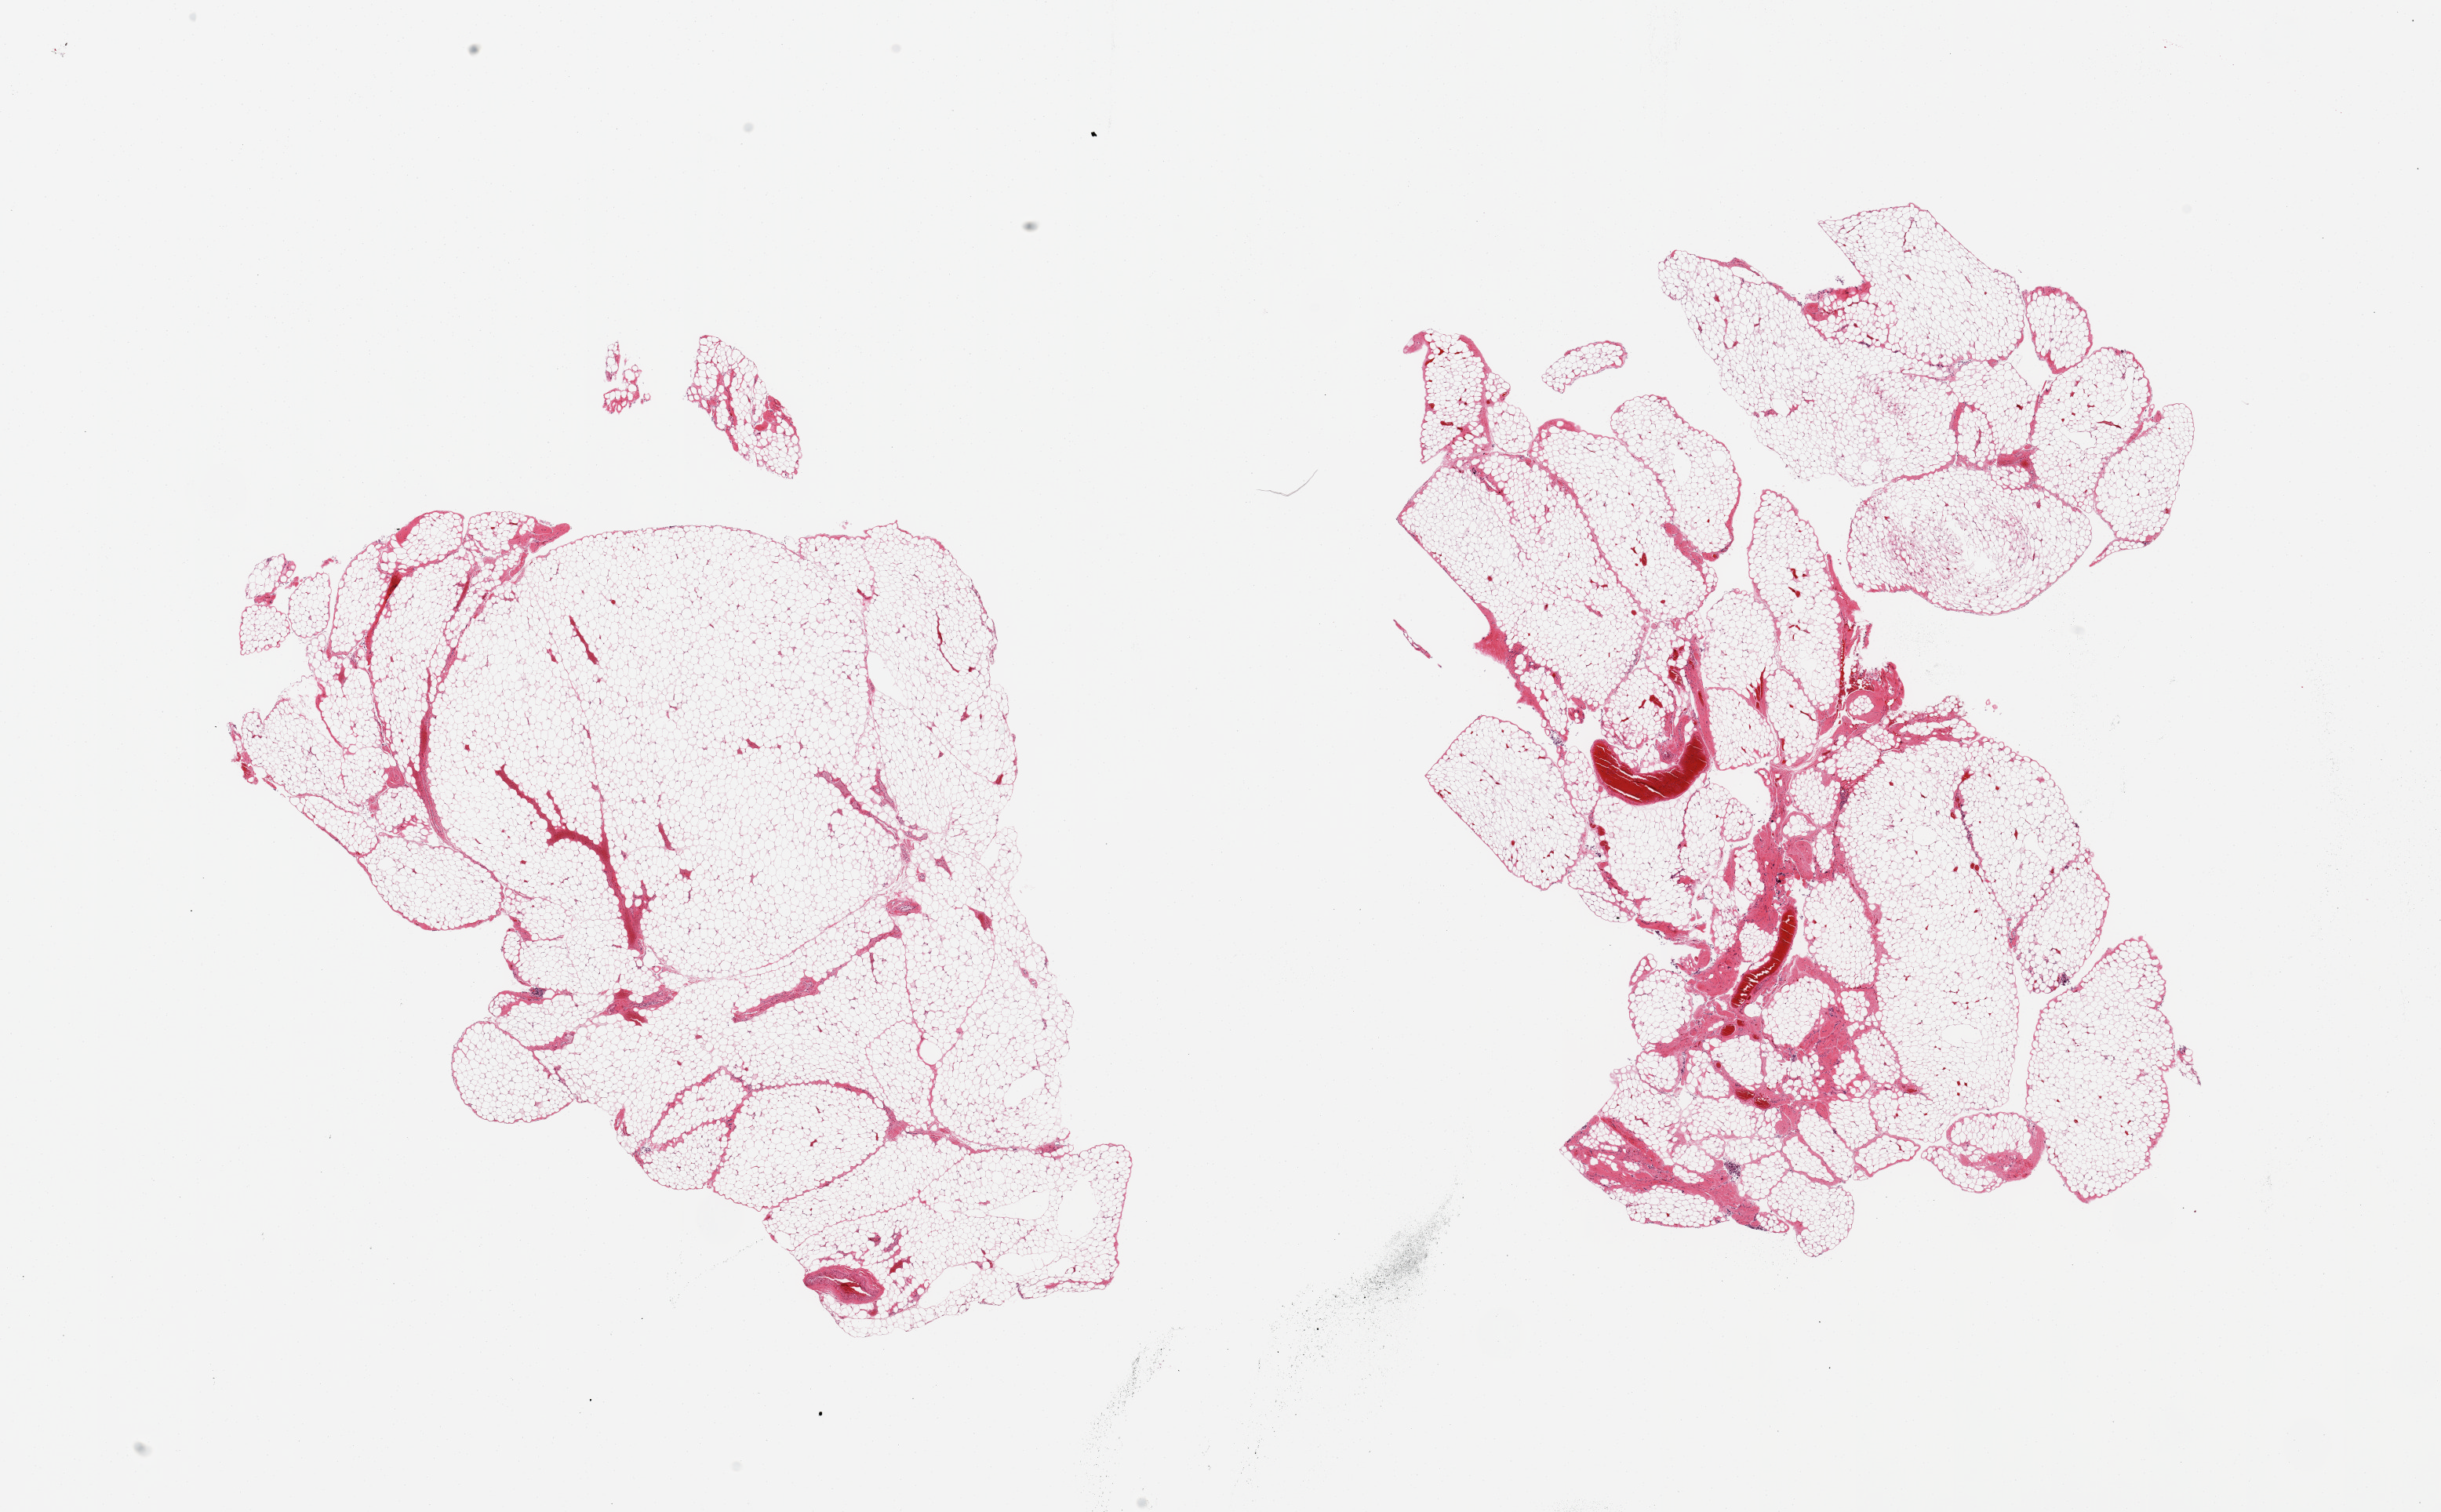
Hematoxylin and eosin (H&E) whole-slide image, shown as a low-resolution overview of the whole scanned area (about 24.6 x 15.2 mm), PAXgene-fixed paraffin-embedded (PFPE) section, sampled site (target tissue): omentum, donor tissue sample. Male donor.
- reviewer comment on this tissue sample: 2 pieces; lobulated mature fat